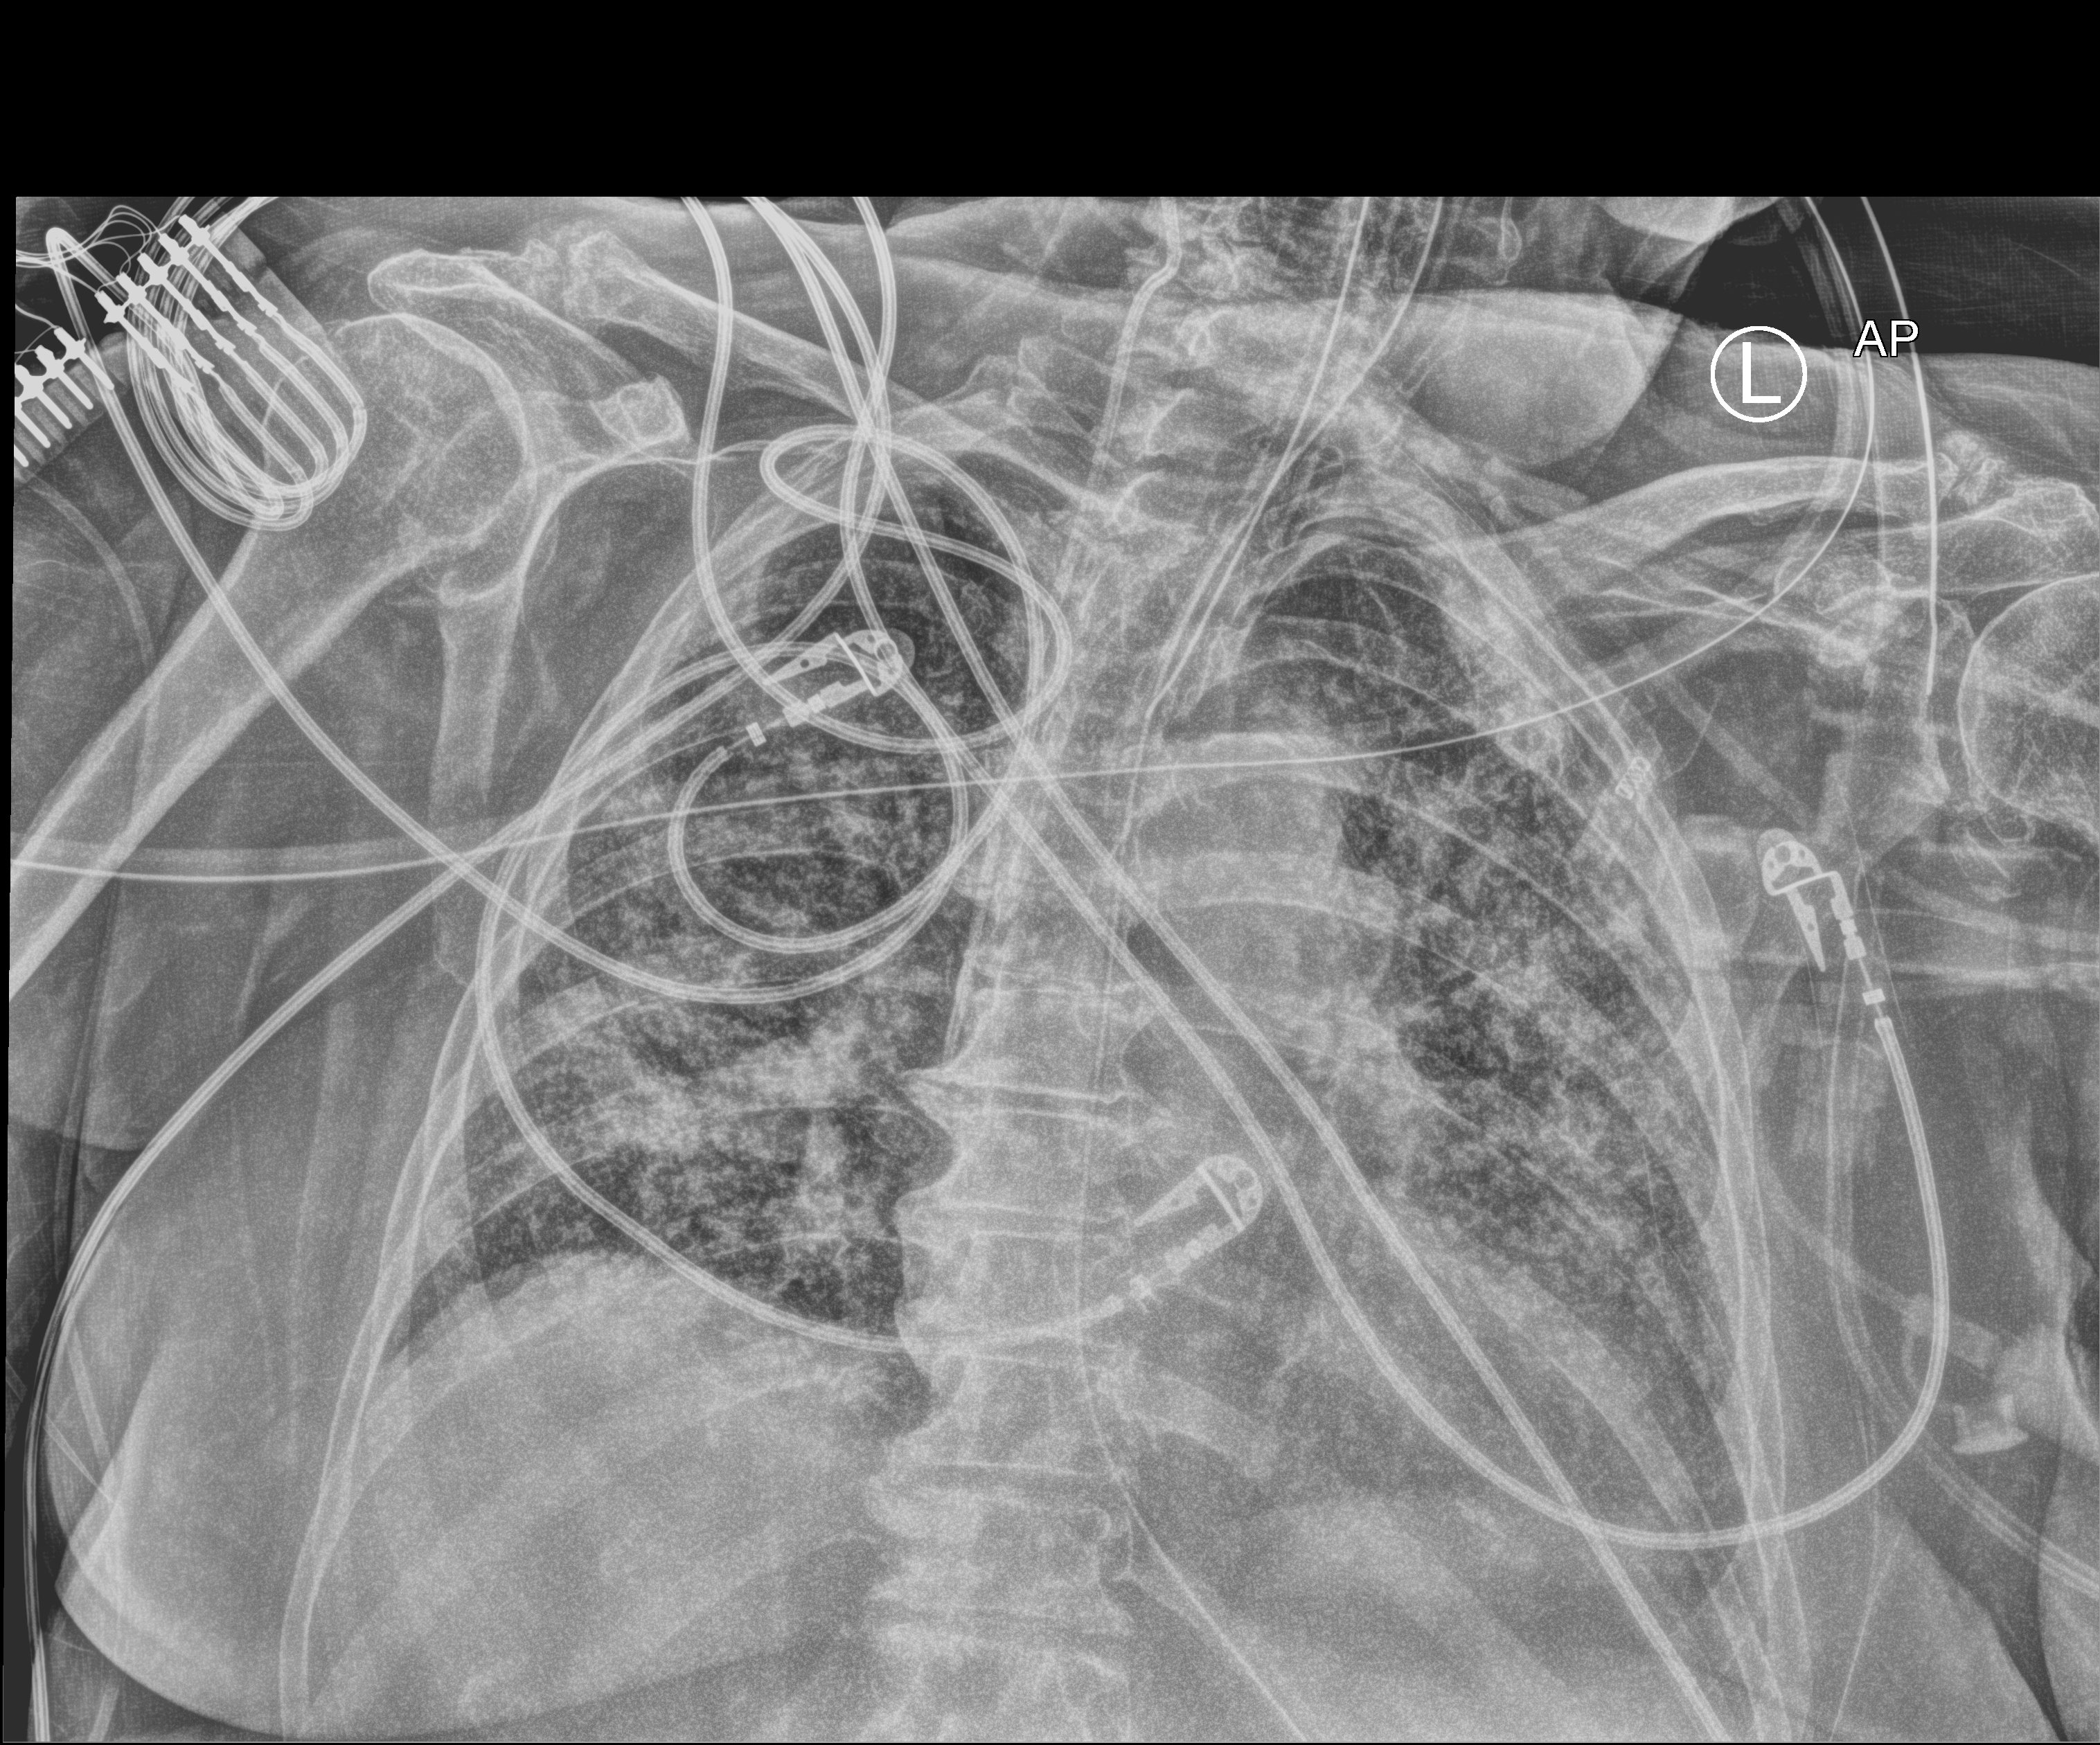
Chest X-ray (portable), anteroposterior (AP) projection. Patient hospitalised with COVID-19; female, aged 75–90 years.
Admission-level facts for this patient (not findings on this image; timing relative to this image not recorded):
- diabetes (admission record): no
- mechanically ventilated during this hospital stay: yes